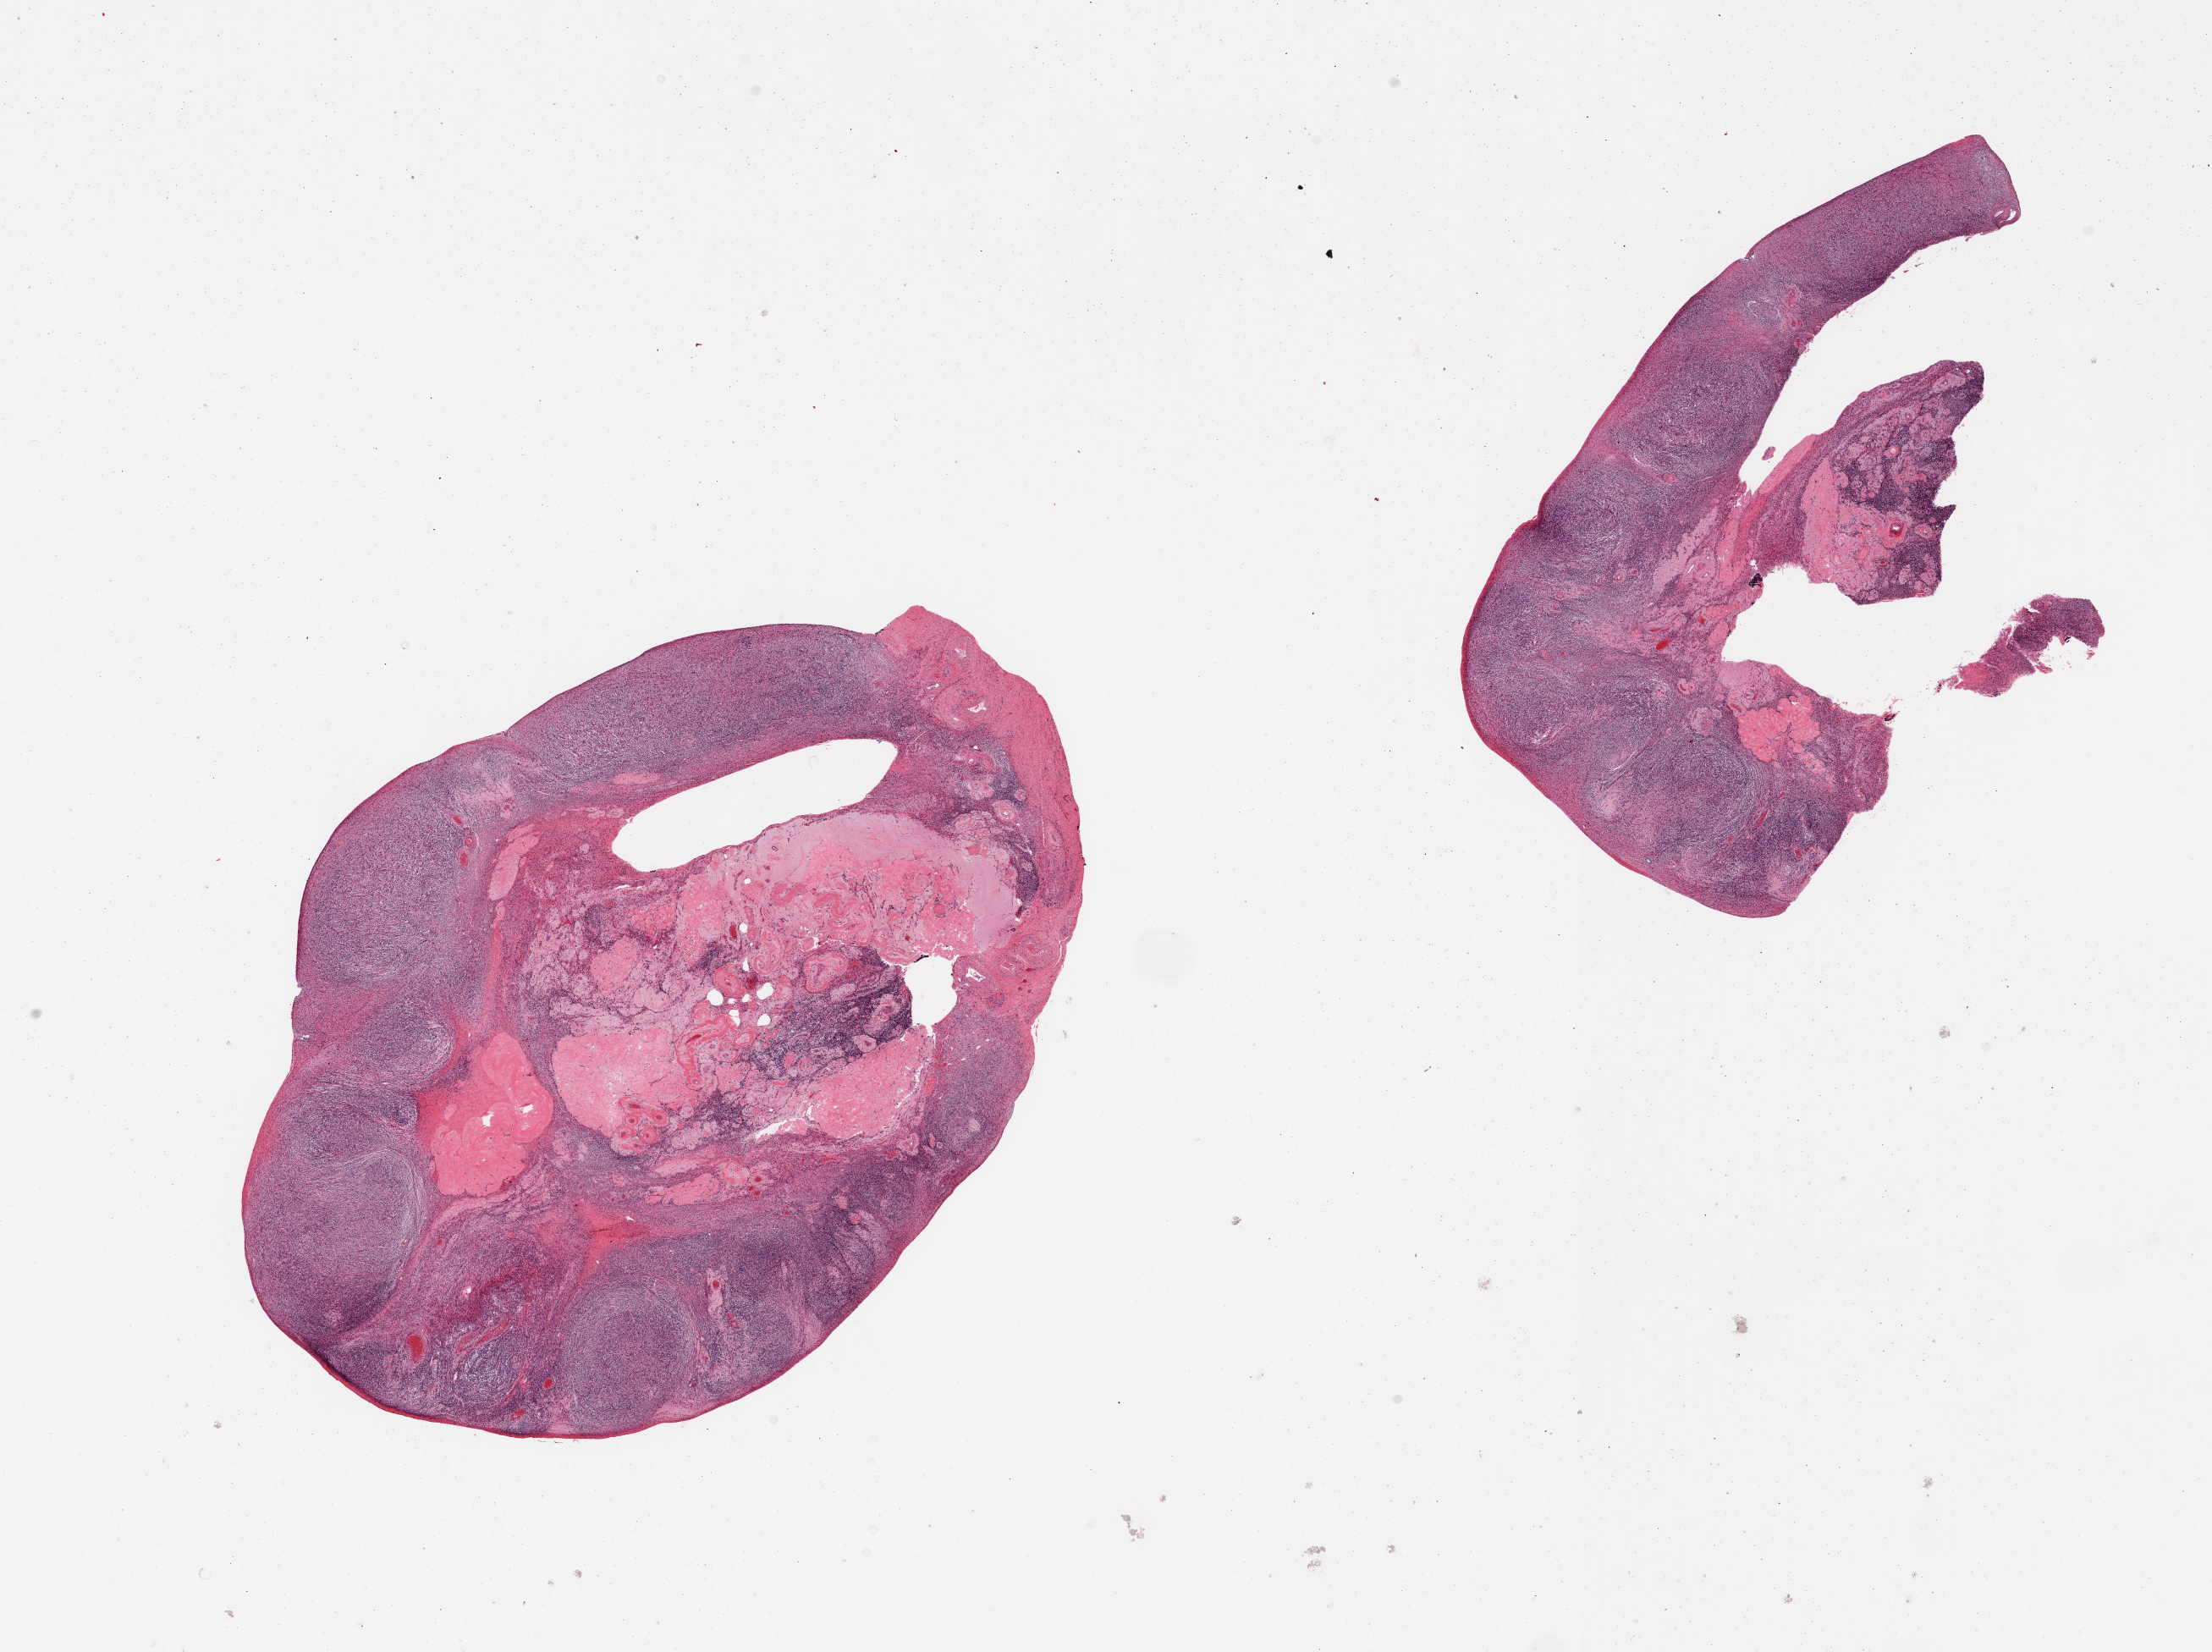
Digitized haematoxylin and eosin-stained section, brightfield, shown as a low-resolution overview of the whole scanned area (about 20.7 x 15.4 mm, acquisition: 20x scan), PAXgene-fixed, paraffin-embedded tissue, target tissue: ovary, tissue donor sample. Donor sex: female.
Pathologist's review note for this sample: 2 pieces; atrophic; corpora albicantia.